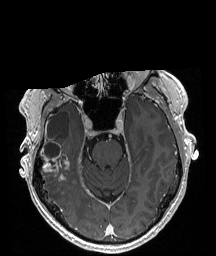
Brain MRI from a brain-tumour surgery series, one axial slice. Slice 132 of 208 in the series (ordered by position). T1-weighted post-contrast. 1 mm slice thickness. 216 × 256 image matrix. From the clinical record (not read from this slice): histopathology: Astrocytoma; WHO grade: 4; IDH mutation: yes; tumour location: Right Temporal.
Outlined on this slice (expert manual segmentation):
- tumour: bounding box <40,141,68,181> (left, top, right, bottom; pixels)